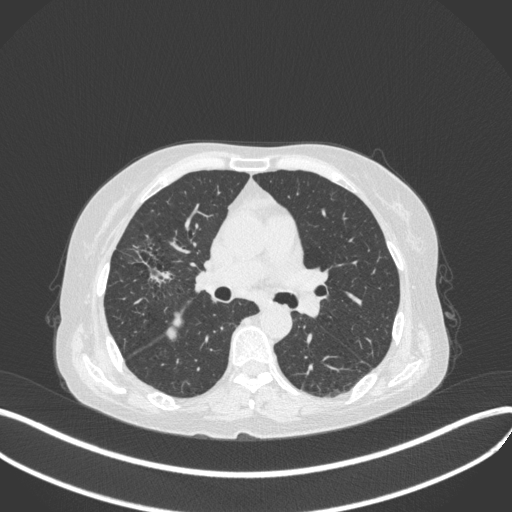
Chest CT, one axial slice; slice 232 of 429 in the series (ordered by position); reconstruction kernel B31f; 120 kVp; lung window (W 1500 / L -600 HU); 1 mm slice thickness; 512 × 512 image matrix. Patient: female, 69 years. Case-level facts recorded for this patient, not image findings: clinical TNM (as recorded): T1b N3 M0.
Outlined on this slice (rectangle marked by the reading radiologist):
- lung tumour (recorded histology: small cell carcinoma): bounding box (x1, y1, x2, y2) in pixels: (125, 229, 175, 291)